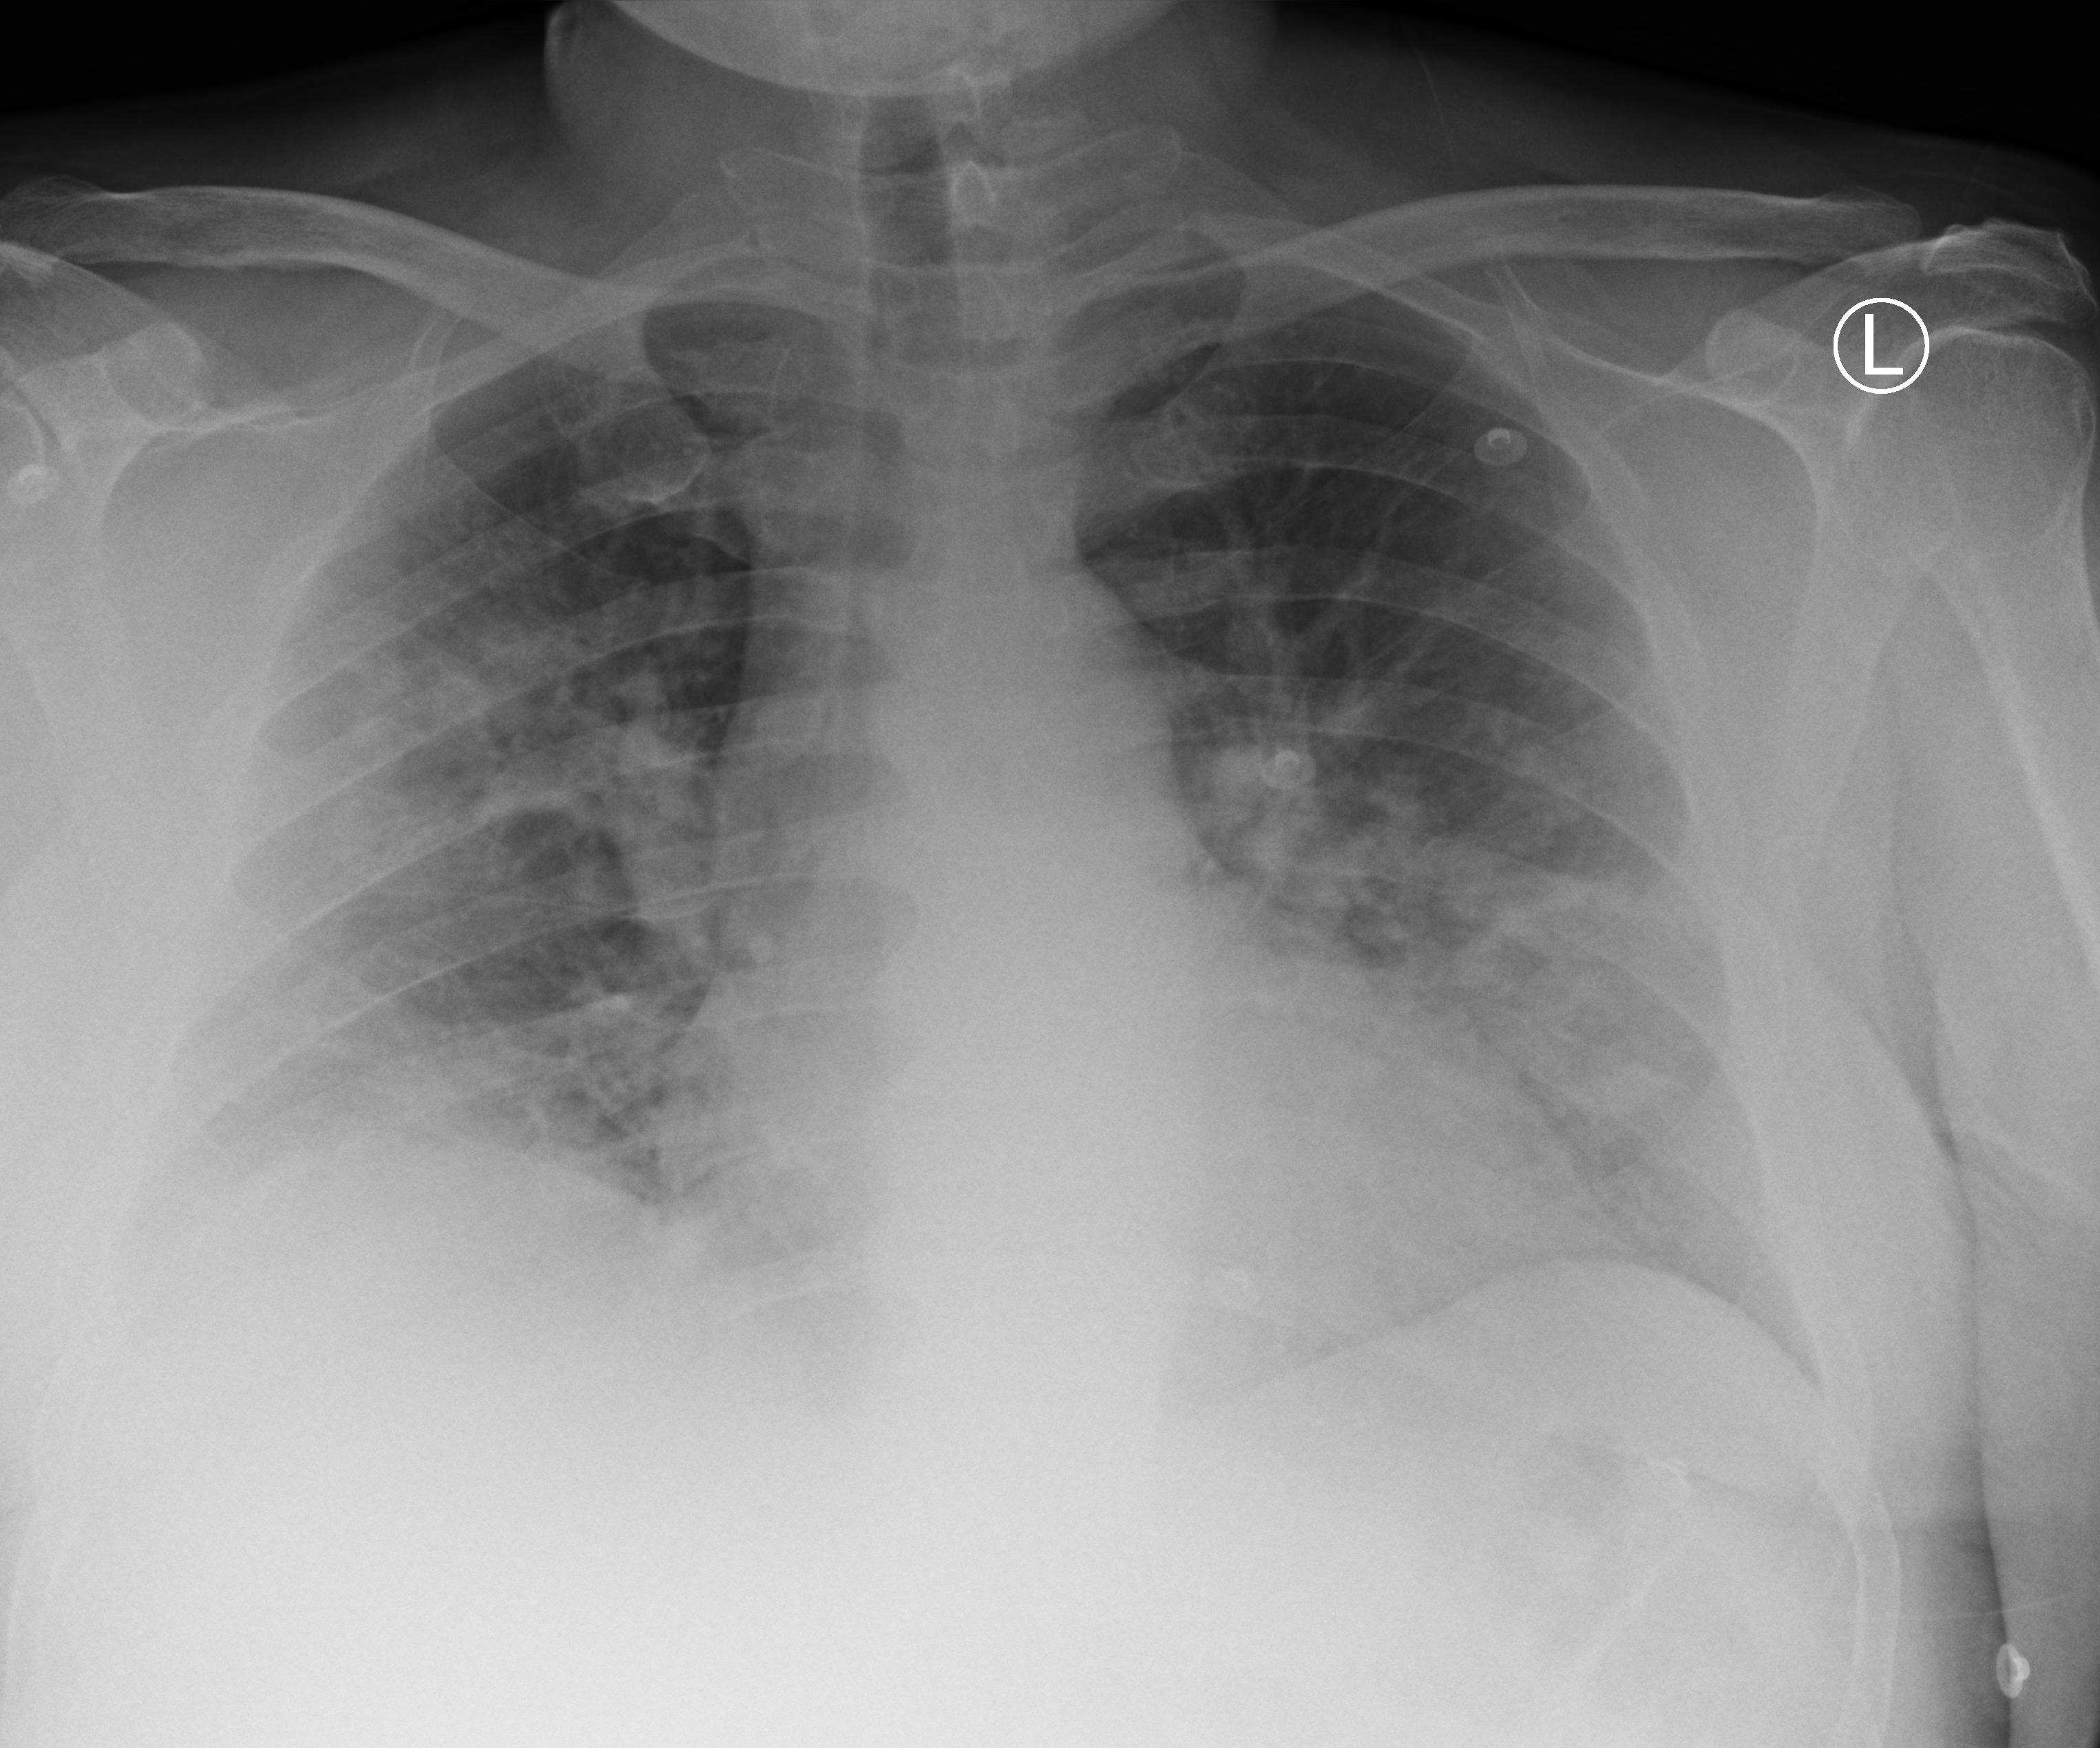
Chest X-ray (portable); anteroposterior (AP) projection. Male patient hospitalised with COVID-19, age 18–59 years.
Hospital-stay facts (about this admission, not read from this image; timing relative to this image not recorded): mechanically ventilated during this hospital stay: no; chronic kidney disease (admission record): yes; admitted to intensive care during this hospital stay: no.